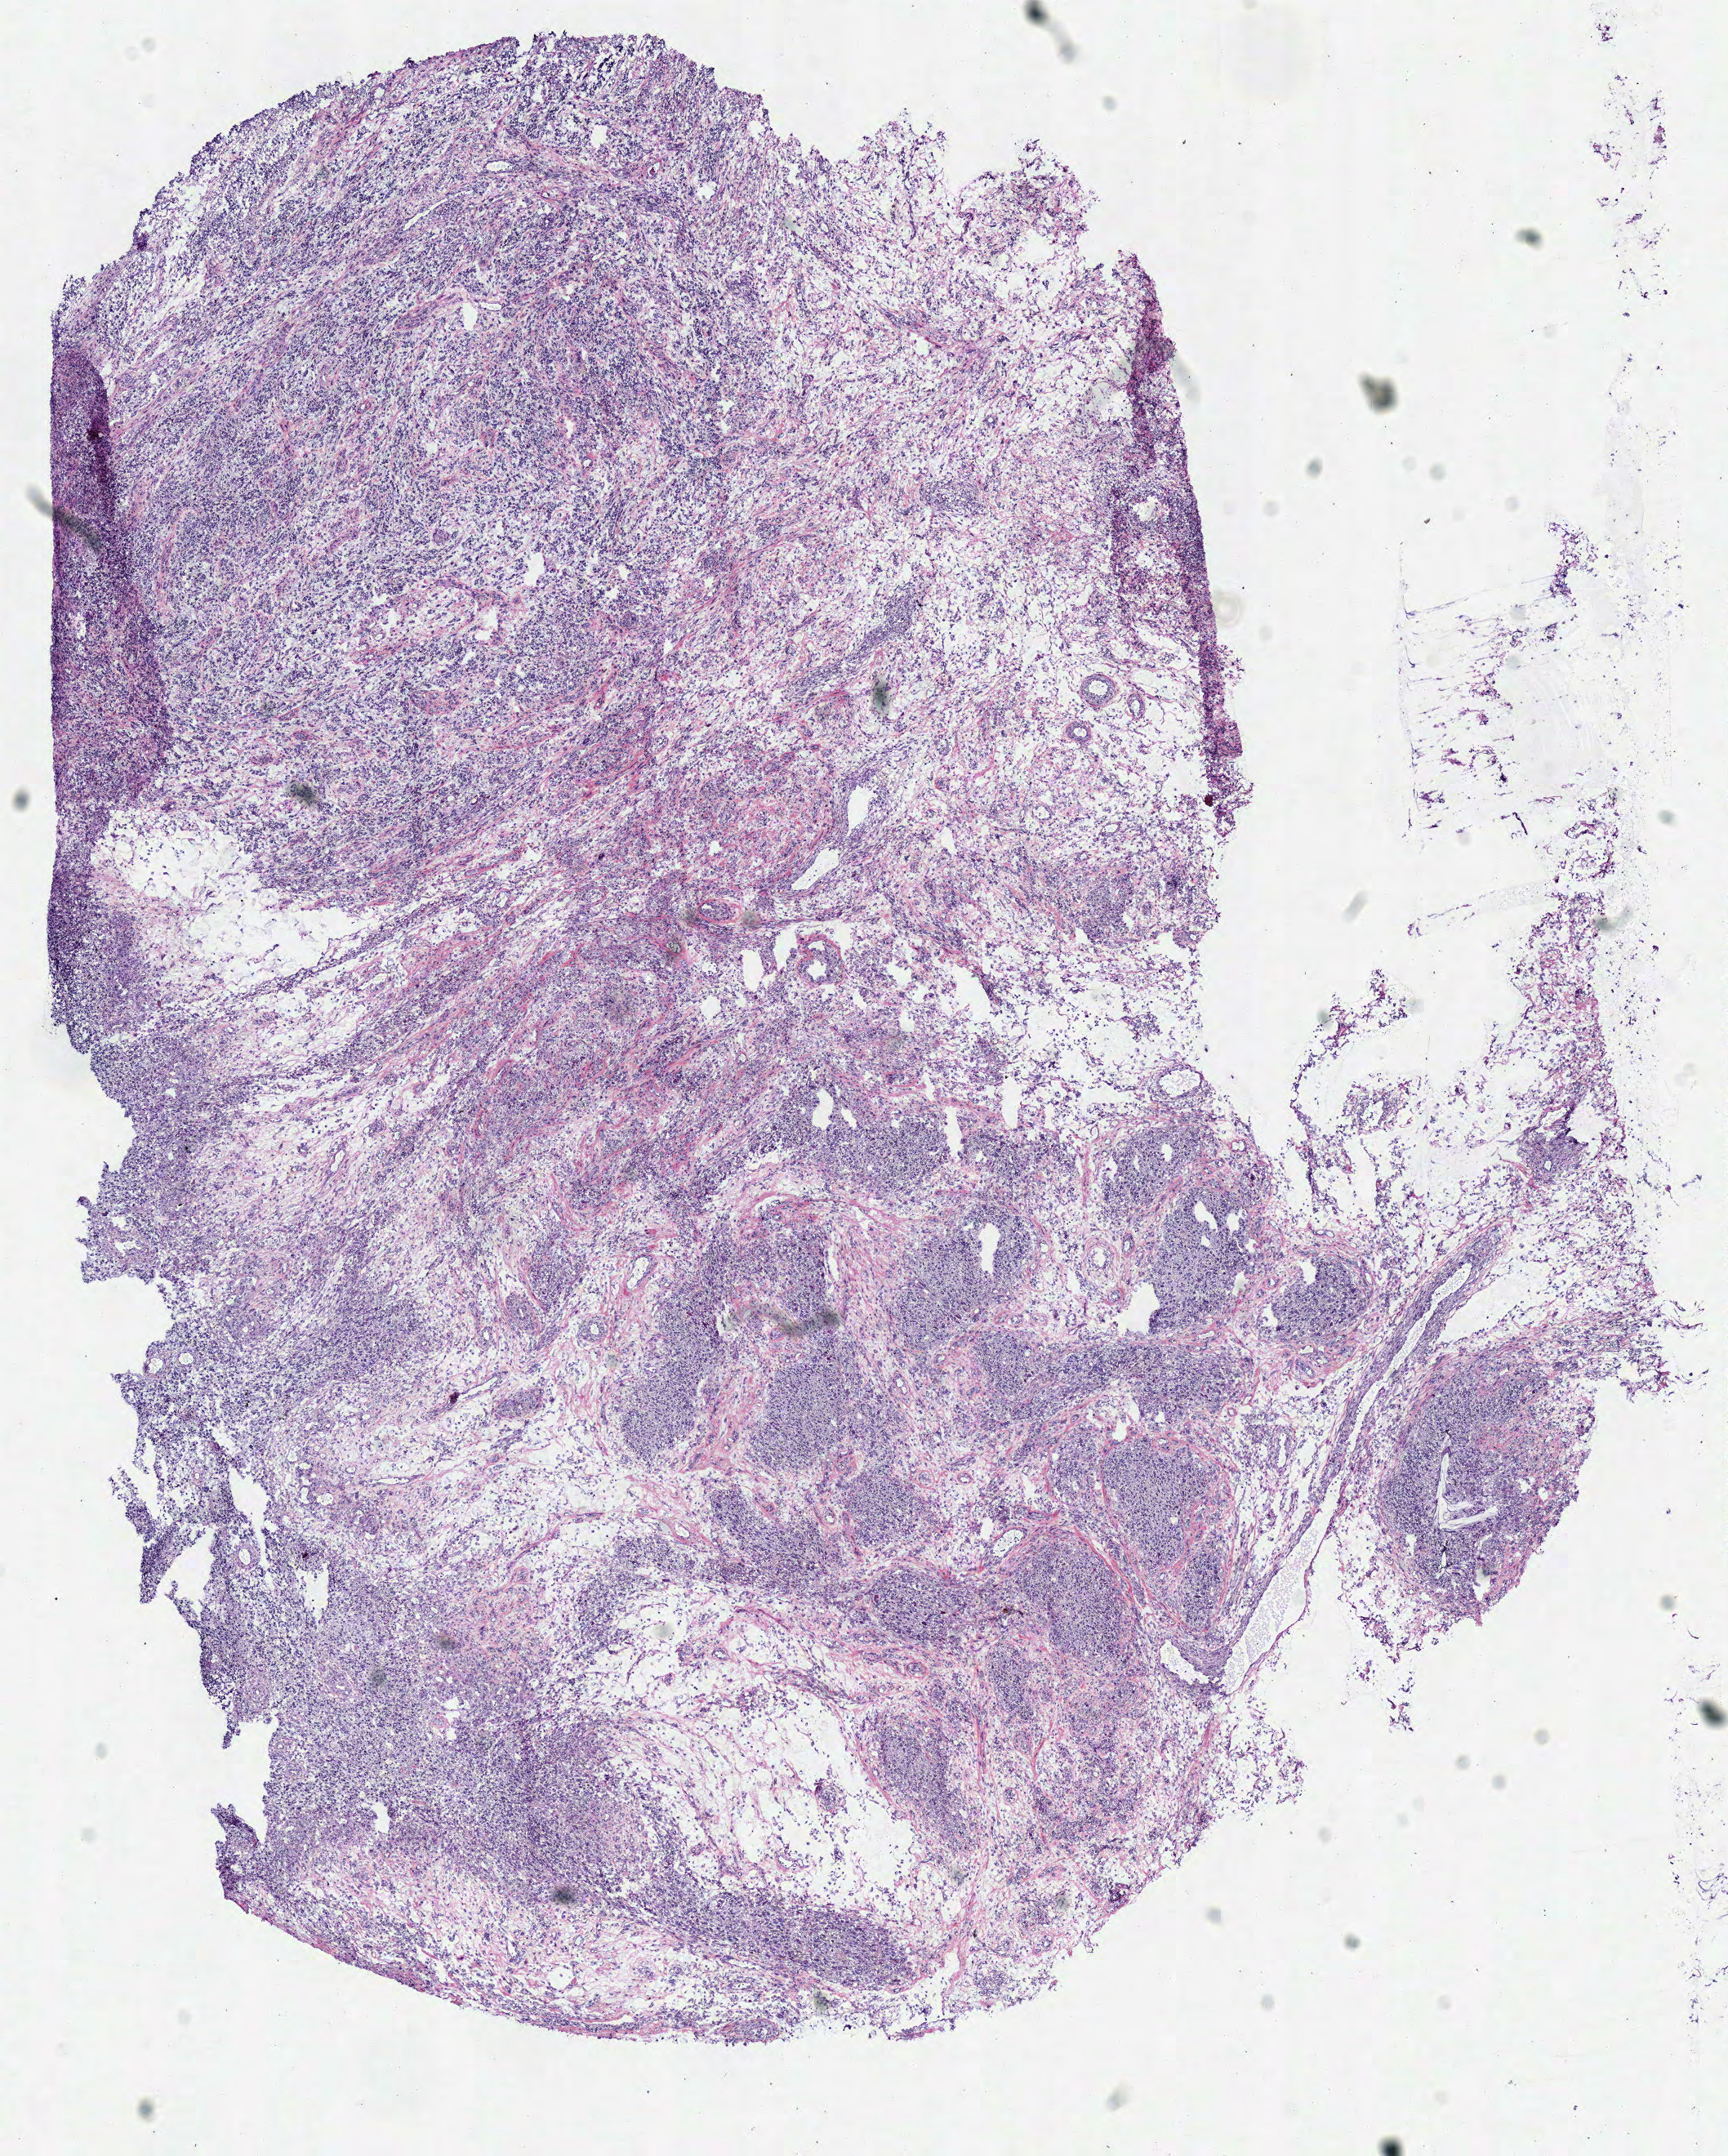
Whole-slide histology image, H&E-stained — shown as a low-resolution overview of the whole scanned area (about 8.3 x 10.4 mm); frozen section; primary tumour sample from the brain. Female patient; age at initial diagnosis 76 years. Pathologist review of this section (percent, as recorded): tumour cells 100%, tumour nuclei 80%, normal cells 0%, stromal cells 0%, necrosis 0%.
Histologic diagnosis: Glioblastoma.